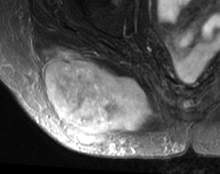
MRI of an extremity soft-tissue mass, one axial slice. Position 23 of 63 along the scan axis. T2-weighted fat-saturated. MR volume resampled by the dataset authors to the PET/CT grid (not the native acquisition matrix). 3.27 mm slice thickness. 220 × 174 image matrix, field of view 215 × 170 mm. Female patient. From the clinical record (not read from this slice): histological type: spindle cell suggestive of myxofibrosarcoma; grade: intermediate; site of the primary tumour: right buttock.
Outlined on this slice (expert contour drawn on MRI and transferred to this co-registered scan by the dataset authors):
- gross tumour volume (mass): box from (x=42, y=47) to (x=151, y=146) px